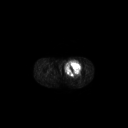
FDG PET of an extremity soft-tissue mass (from a PET/CT study), one axial slice. 3.27 mm slice thickness. 128 × 128 image matrix. Male patient, age 63 years. Case-level facts recorded for this patient, not image findings: histological type: pleiomorphic liposarcoma; grade: high; site of the primary tumour: left thigh.
Annotated regions visible in this slice (expert contour drawn on MRI and transferred to this co-registered scan by the dataset authors):
- gross tumour volume including surrounding oedema: box from (x=65, y=59) to (x=82, y=75) px
- gross tumour volume (mass): (x=65, y=59)–(x=81, y=76)